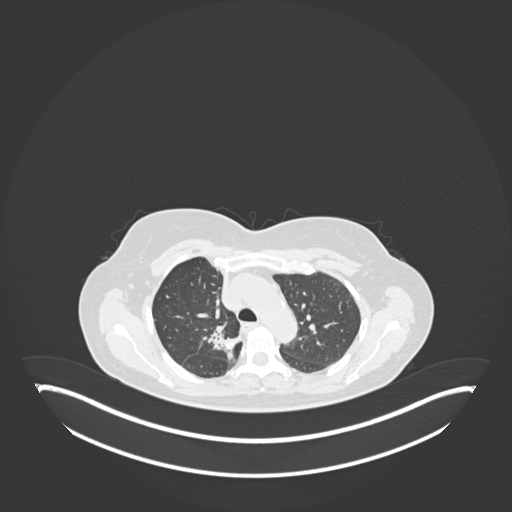
Chest CT, one axial slice; position 128 of 181 along the scan axis; 120 kVp; lung window (W 1500 / L -600 HU); 1 mm slice thickness; 512 × 512 image matrix, field of view 500 × 500 mm. Female patient, age 65 years. Case-level facts recorded for this patient, not image findings: clinical TNM (as recorded): T1b N0 M0.
Structures marked on this image (rectangle marked by the reading radiologist):
- lung tumour (recorded histology: adenocarcinoma): bounding box <208,328,246,366> (left, top, right, bottom; pixels)